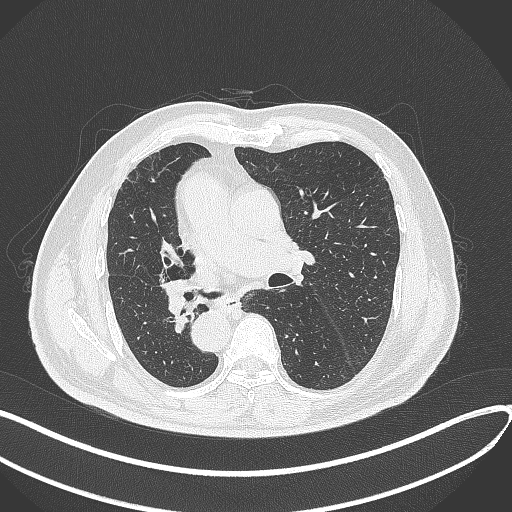
Chest CT, one axial slice; position 156 of 300 along the scan axis; reconstruction kernel B70f; lung window (W 1500 / L -600 HU); 512 × 512 image matrix, field of view 400 × 400 mm. Male patient, age 67 years. Case-level facts recorded for this patient, not image findings: clinical TNM (as recorded): T2a N0 M0.
Outlined on this slice (rectangle marked by the reading radiologist):
- lung tumour (recorded histology: squamous cell carcinoma): box from (x=155, y=275) to (x=188, y=315) px